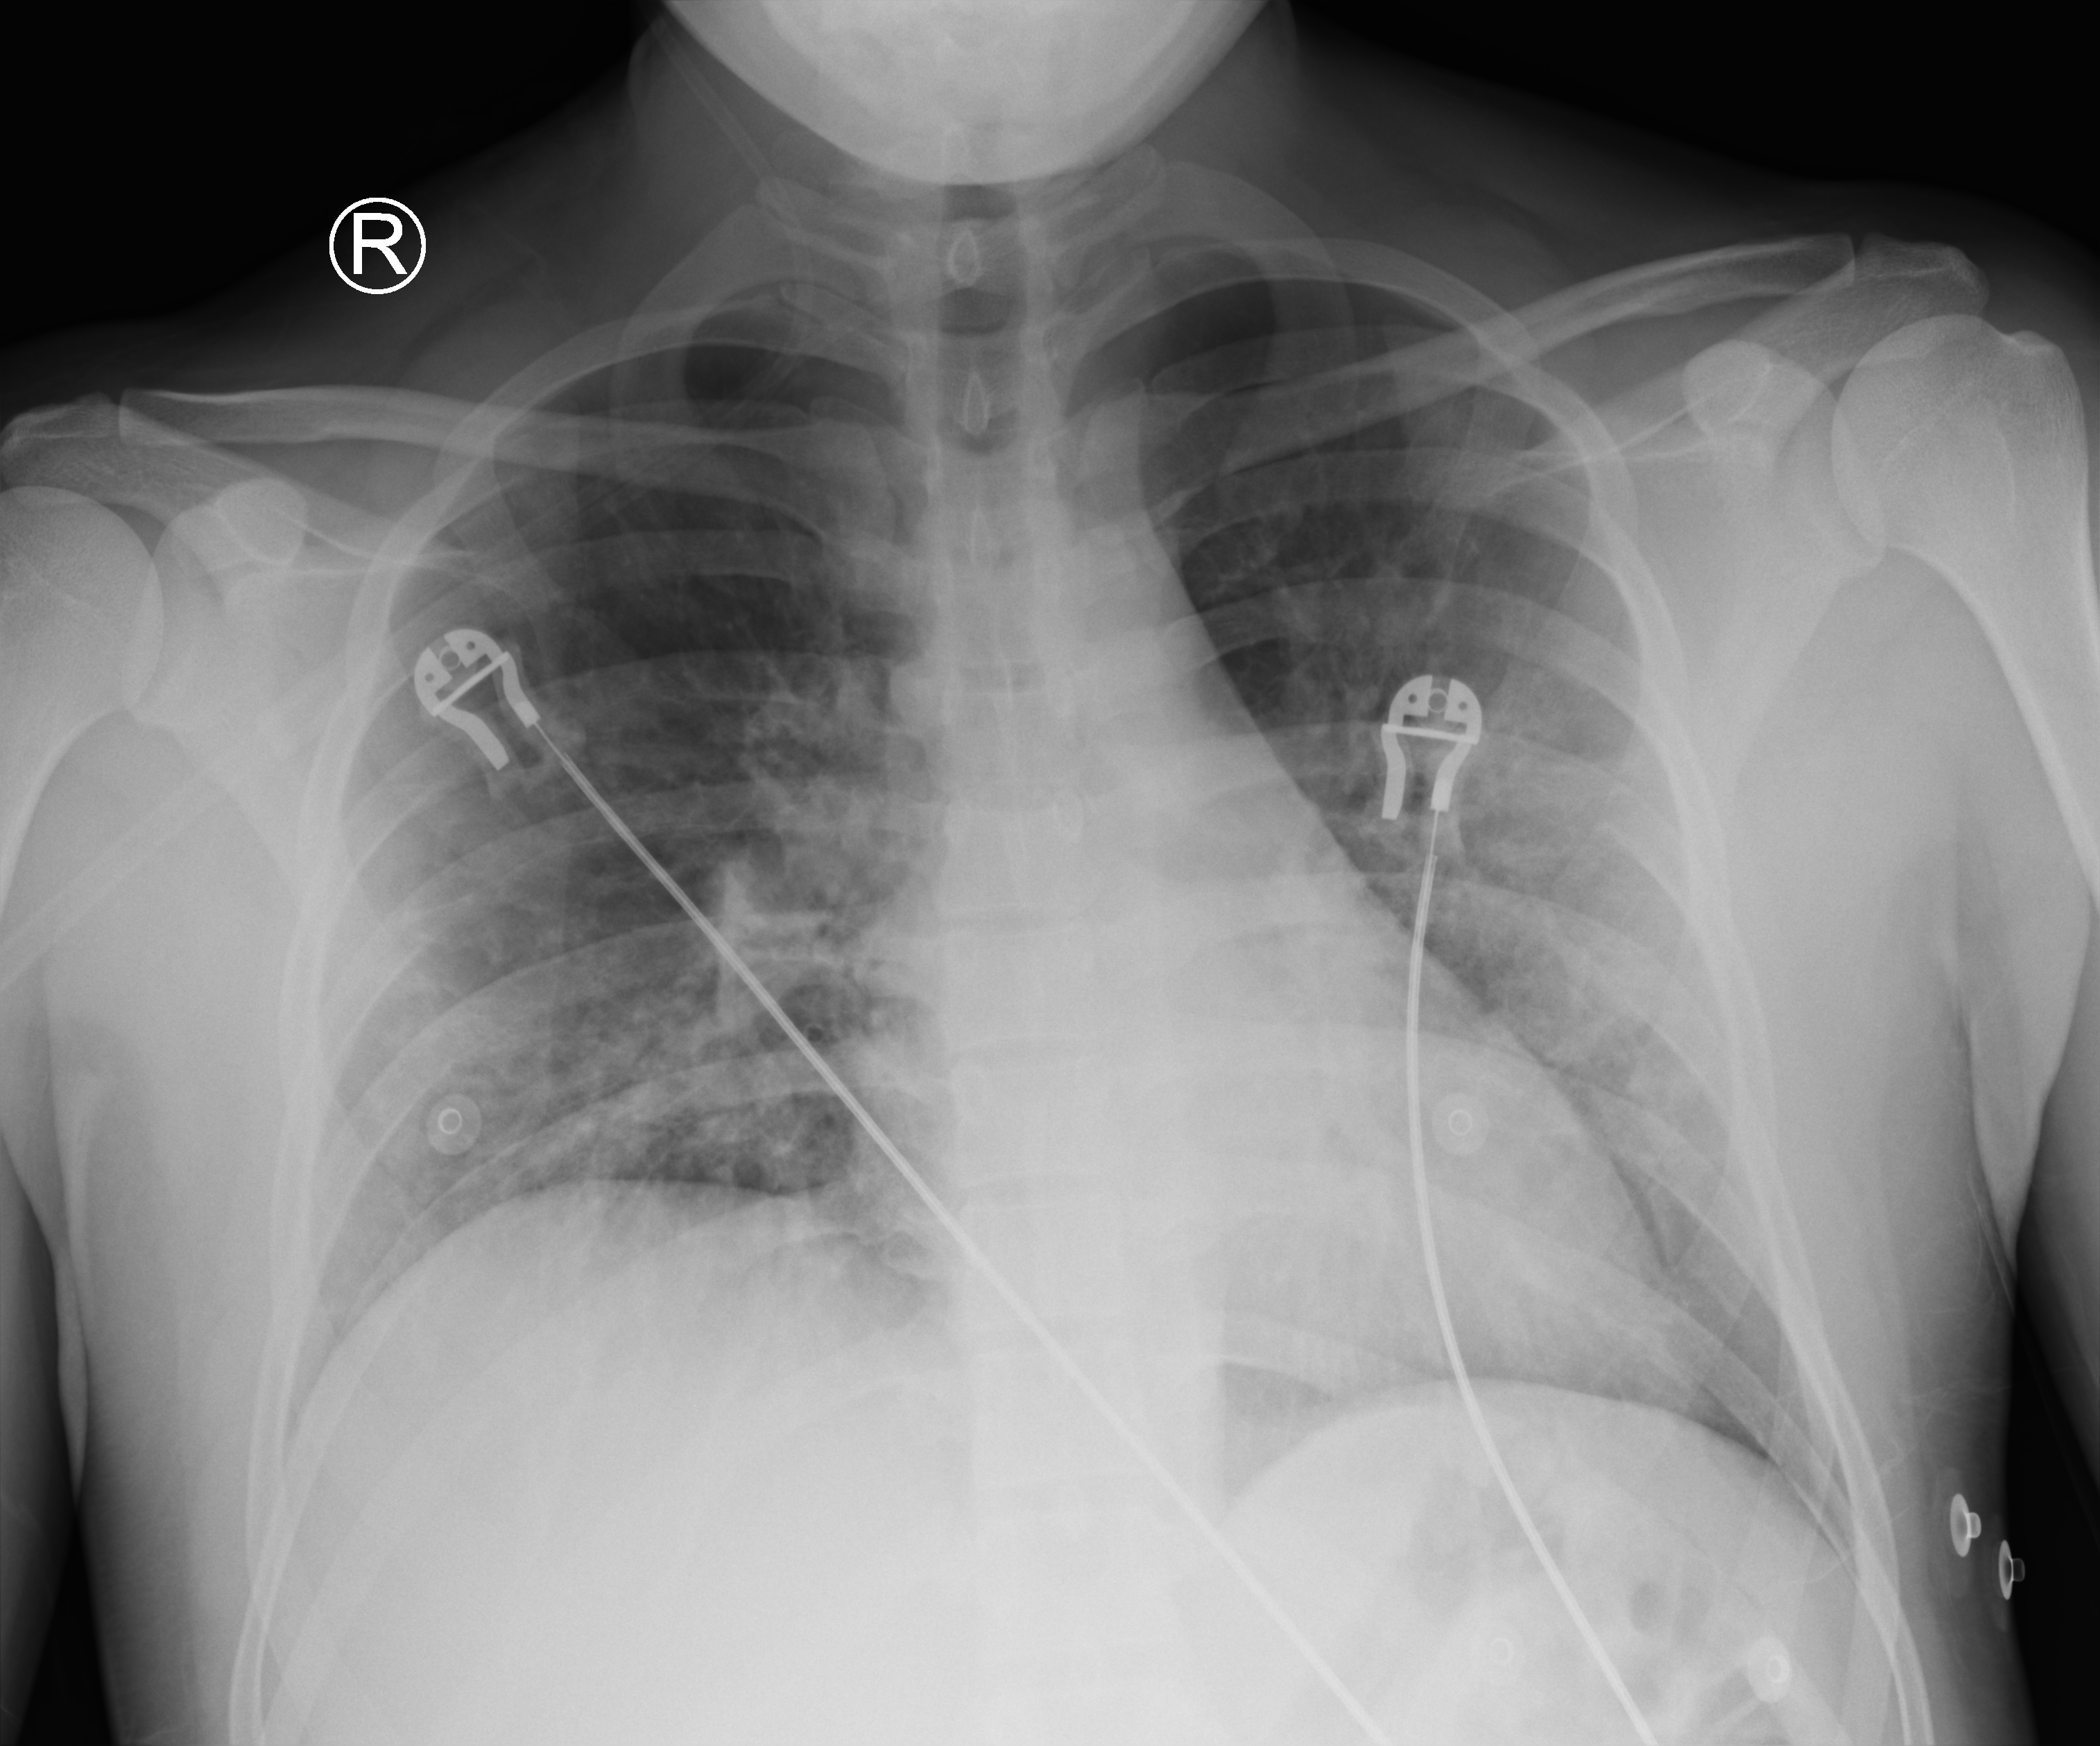
Bedside chest radiograph (computed radiography); anteroposterior (AP) projection. Patient hospitalised with COVID-19; male, aged 18–59 years.
Admission-level facts for this patient (not findings on this image; timing relative to this image not recorded):
- length of hospital stay: 23 days